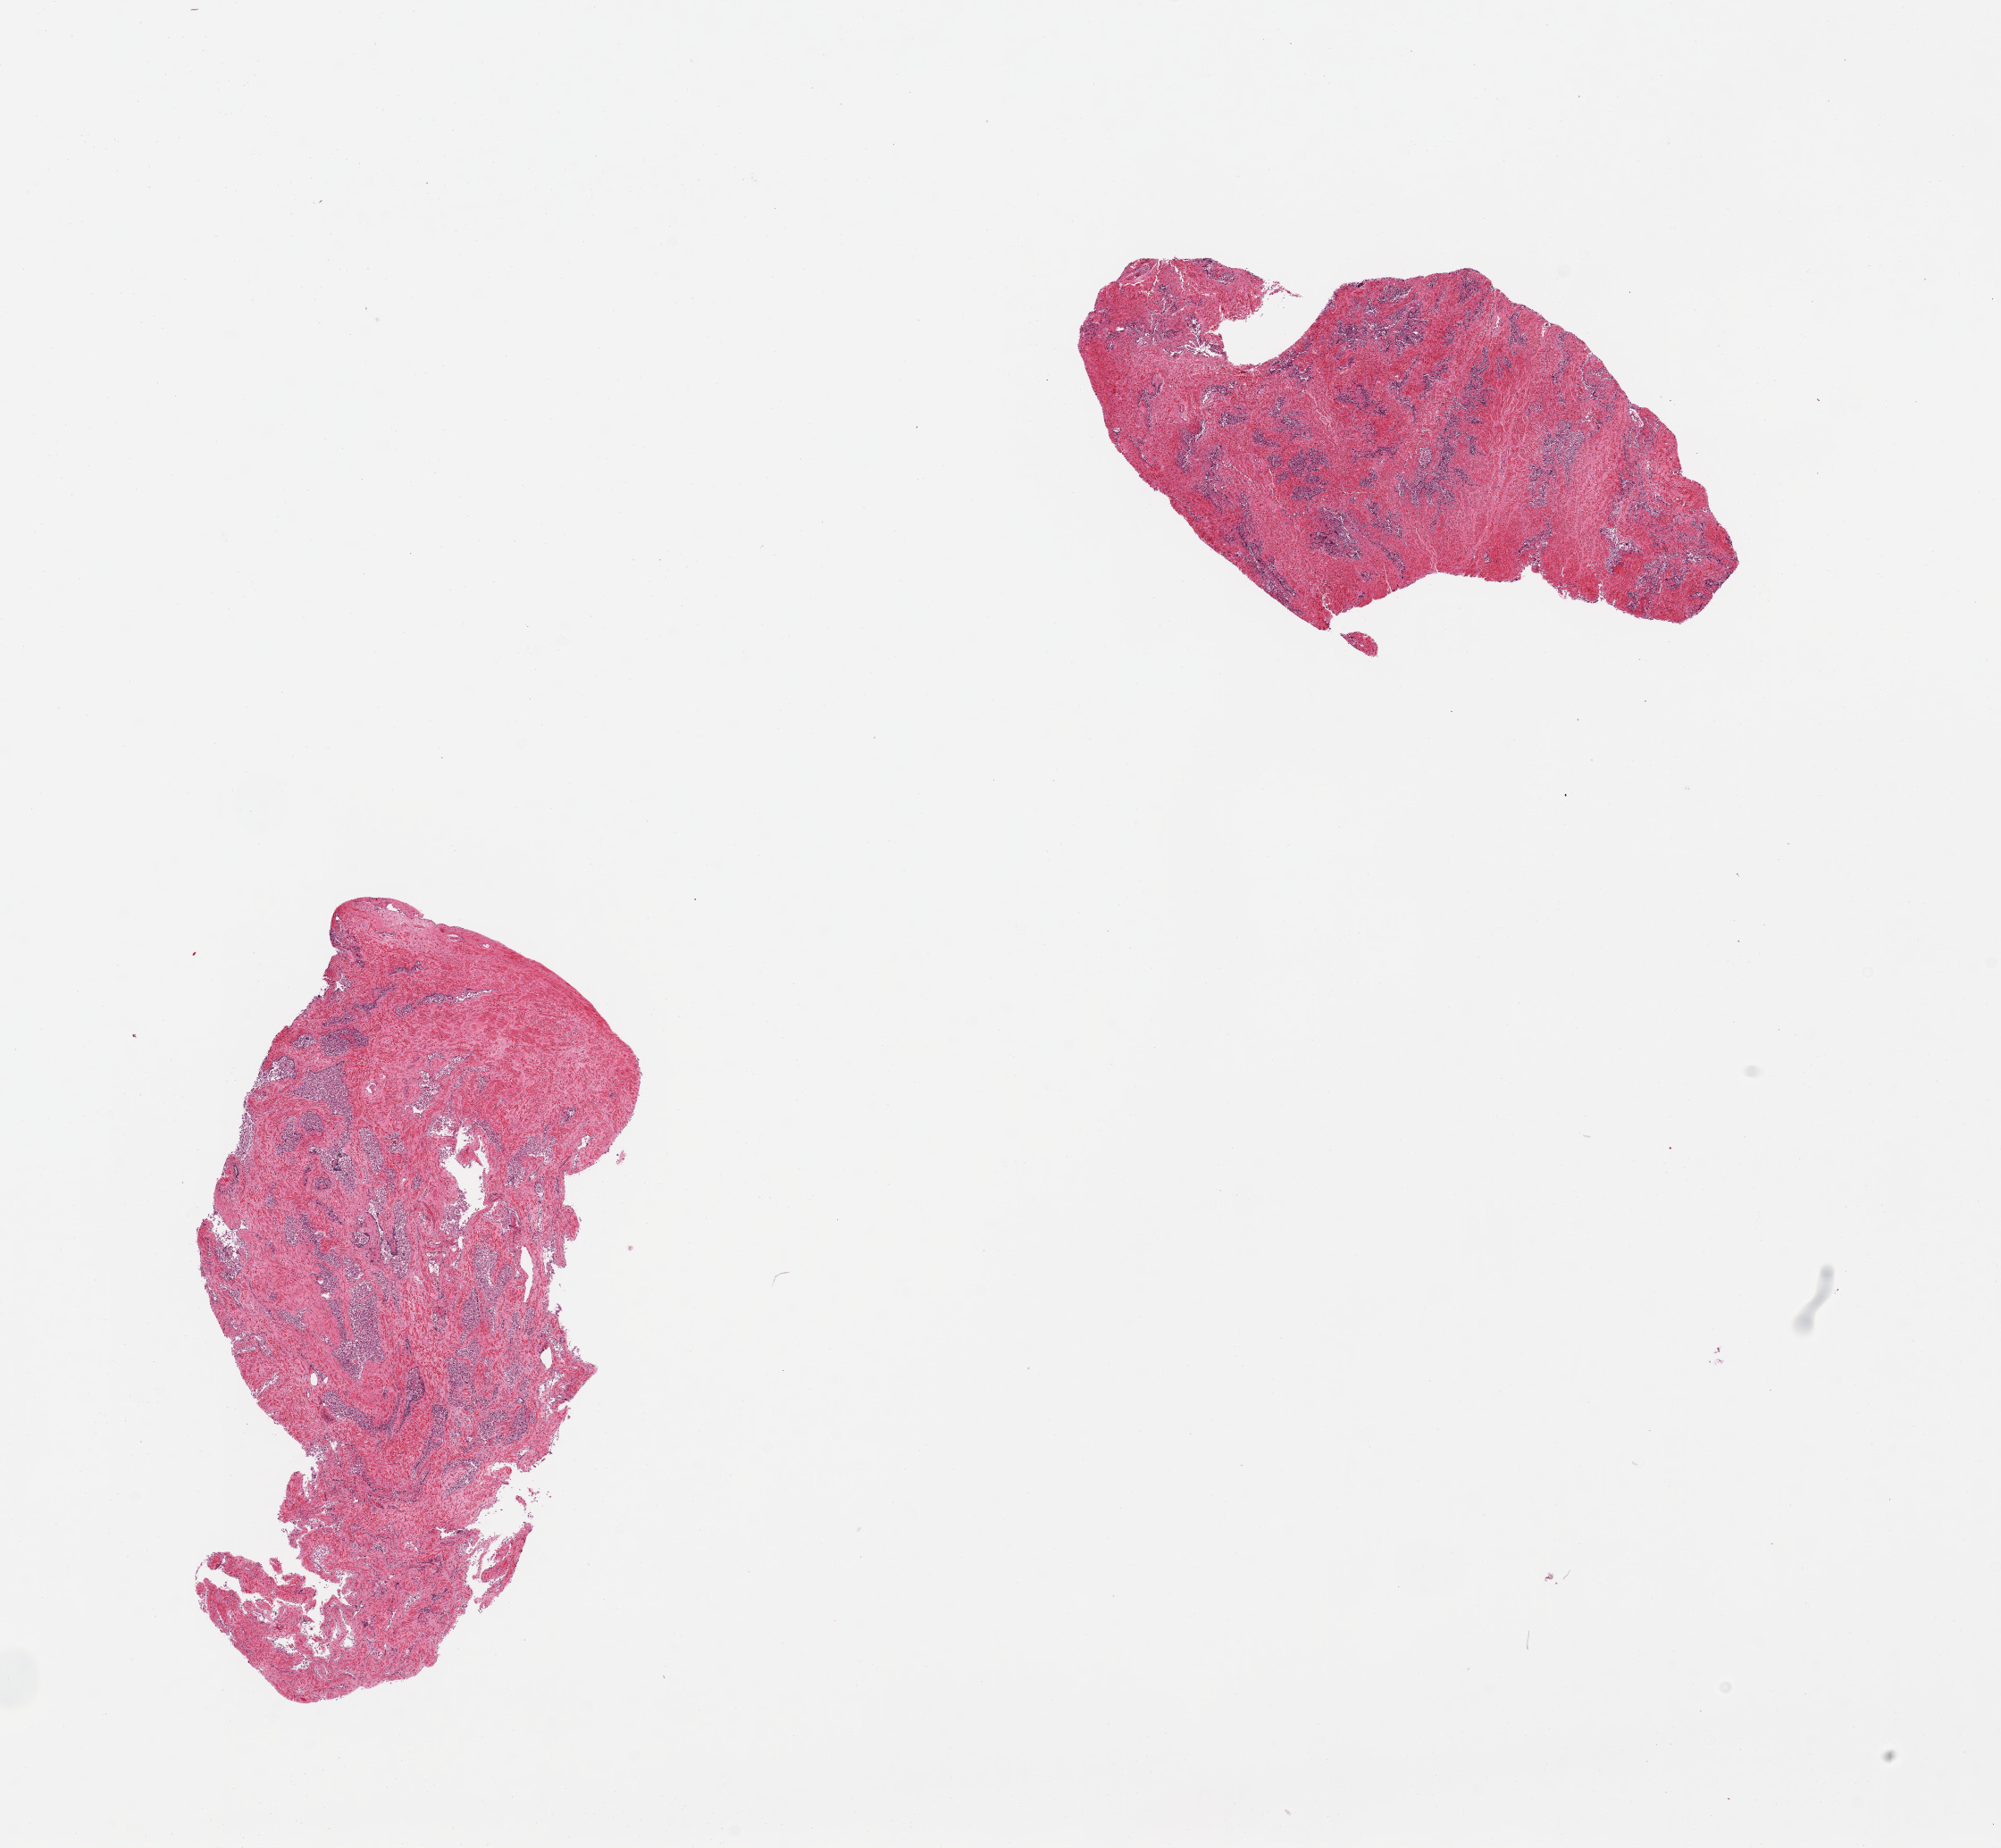
Hematoxylin and eosin (H&E) whole-slide image, a low-resolution overview of the entire scanned area, about 17.7 x 16.4 mm. PAXgene-fixed, paraffin-embedded tissue. Sampled site (target tissue): prostate. Donor tissue sample.
• pathologist's review note for this sample: 2 pieces, glands sloughed